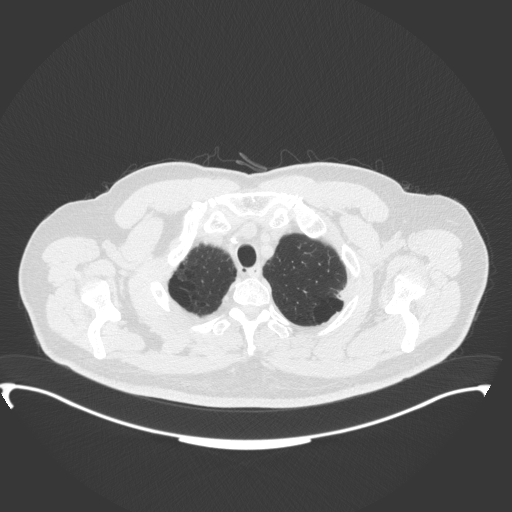
Chest CT, one axial slice. Position 329 of 350 along the scan axis. Reconstruction kernel B31f. 120 kVp. Lung window (W 1500 / L -600 HU). 1 mm slice thickness. 512 × 512 image matrix. Patient: male, 64 years. From the clinical record (not read from this slice): clinical TNM (as recorded): T1c N1 M1.
Outlined on this slice (rectangle marked by the reading radiologist):
- lung tumour (recorded histology: adenocarcinoma): box from (x=335, y=285) to (x=350, y=304) px